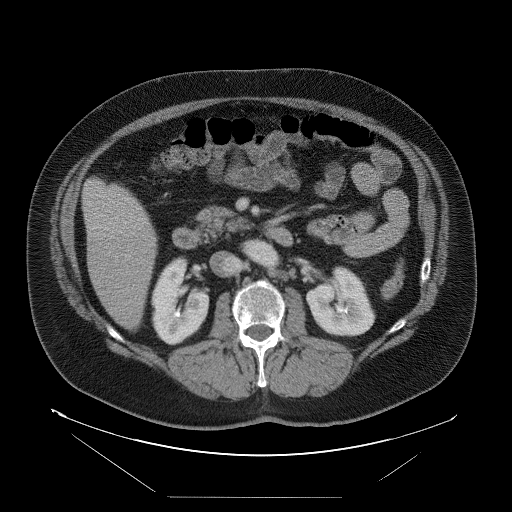
Contrast-enhanced abdominal CT, one axial slice; slice 33 of 114 in the series (ordered by position); intravenous contrast given; soft-tissue window (W 400 / L 40 HU); 5 mm slice thickness; 512 × 512 image matrix. Male patient, age 61 years. Case-level facts recorded for this patient, not image findings: diagnosis: colorectal cancer liver metastases, imaged before liver resection; multiple liver metastases: no; largest metastasis: 6.5 cm; disease in both lobes: yes.
Annotated regions visible in this slice (manually delineated by an expert):
- liver: bounding box [x1, y1, x2, y2] px = [84, 179, 158, 330]